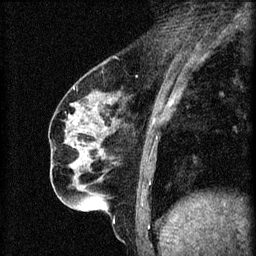
Breast MRI (dynamic contrast-enhanced), one sagittal slice; slice 23 of 60 in the series (ordered by position); 3 images stored at this slice position (order not interpretable as contrast timing); 1.5 T; TE 4.2 ms, TR 8.2 ms; 256 × 256 image matrix, field of view 180 × 180 mm. Female patient, age 56 years.
Structures marked on this image (semi-automatic segmentation, software-assisted and operator-edited):
- analysis volume of interest (the breast-tissue region the enhancement analysis was run in; not a lesion): bounding box <67,136,109,179> (left, top, right, bottom; pixels)
- tumour enhancement mask (voxels above the 70 % enhancement threshold inside the analysis volume of interest): <82,154,84,157>